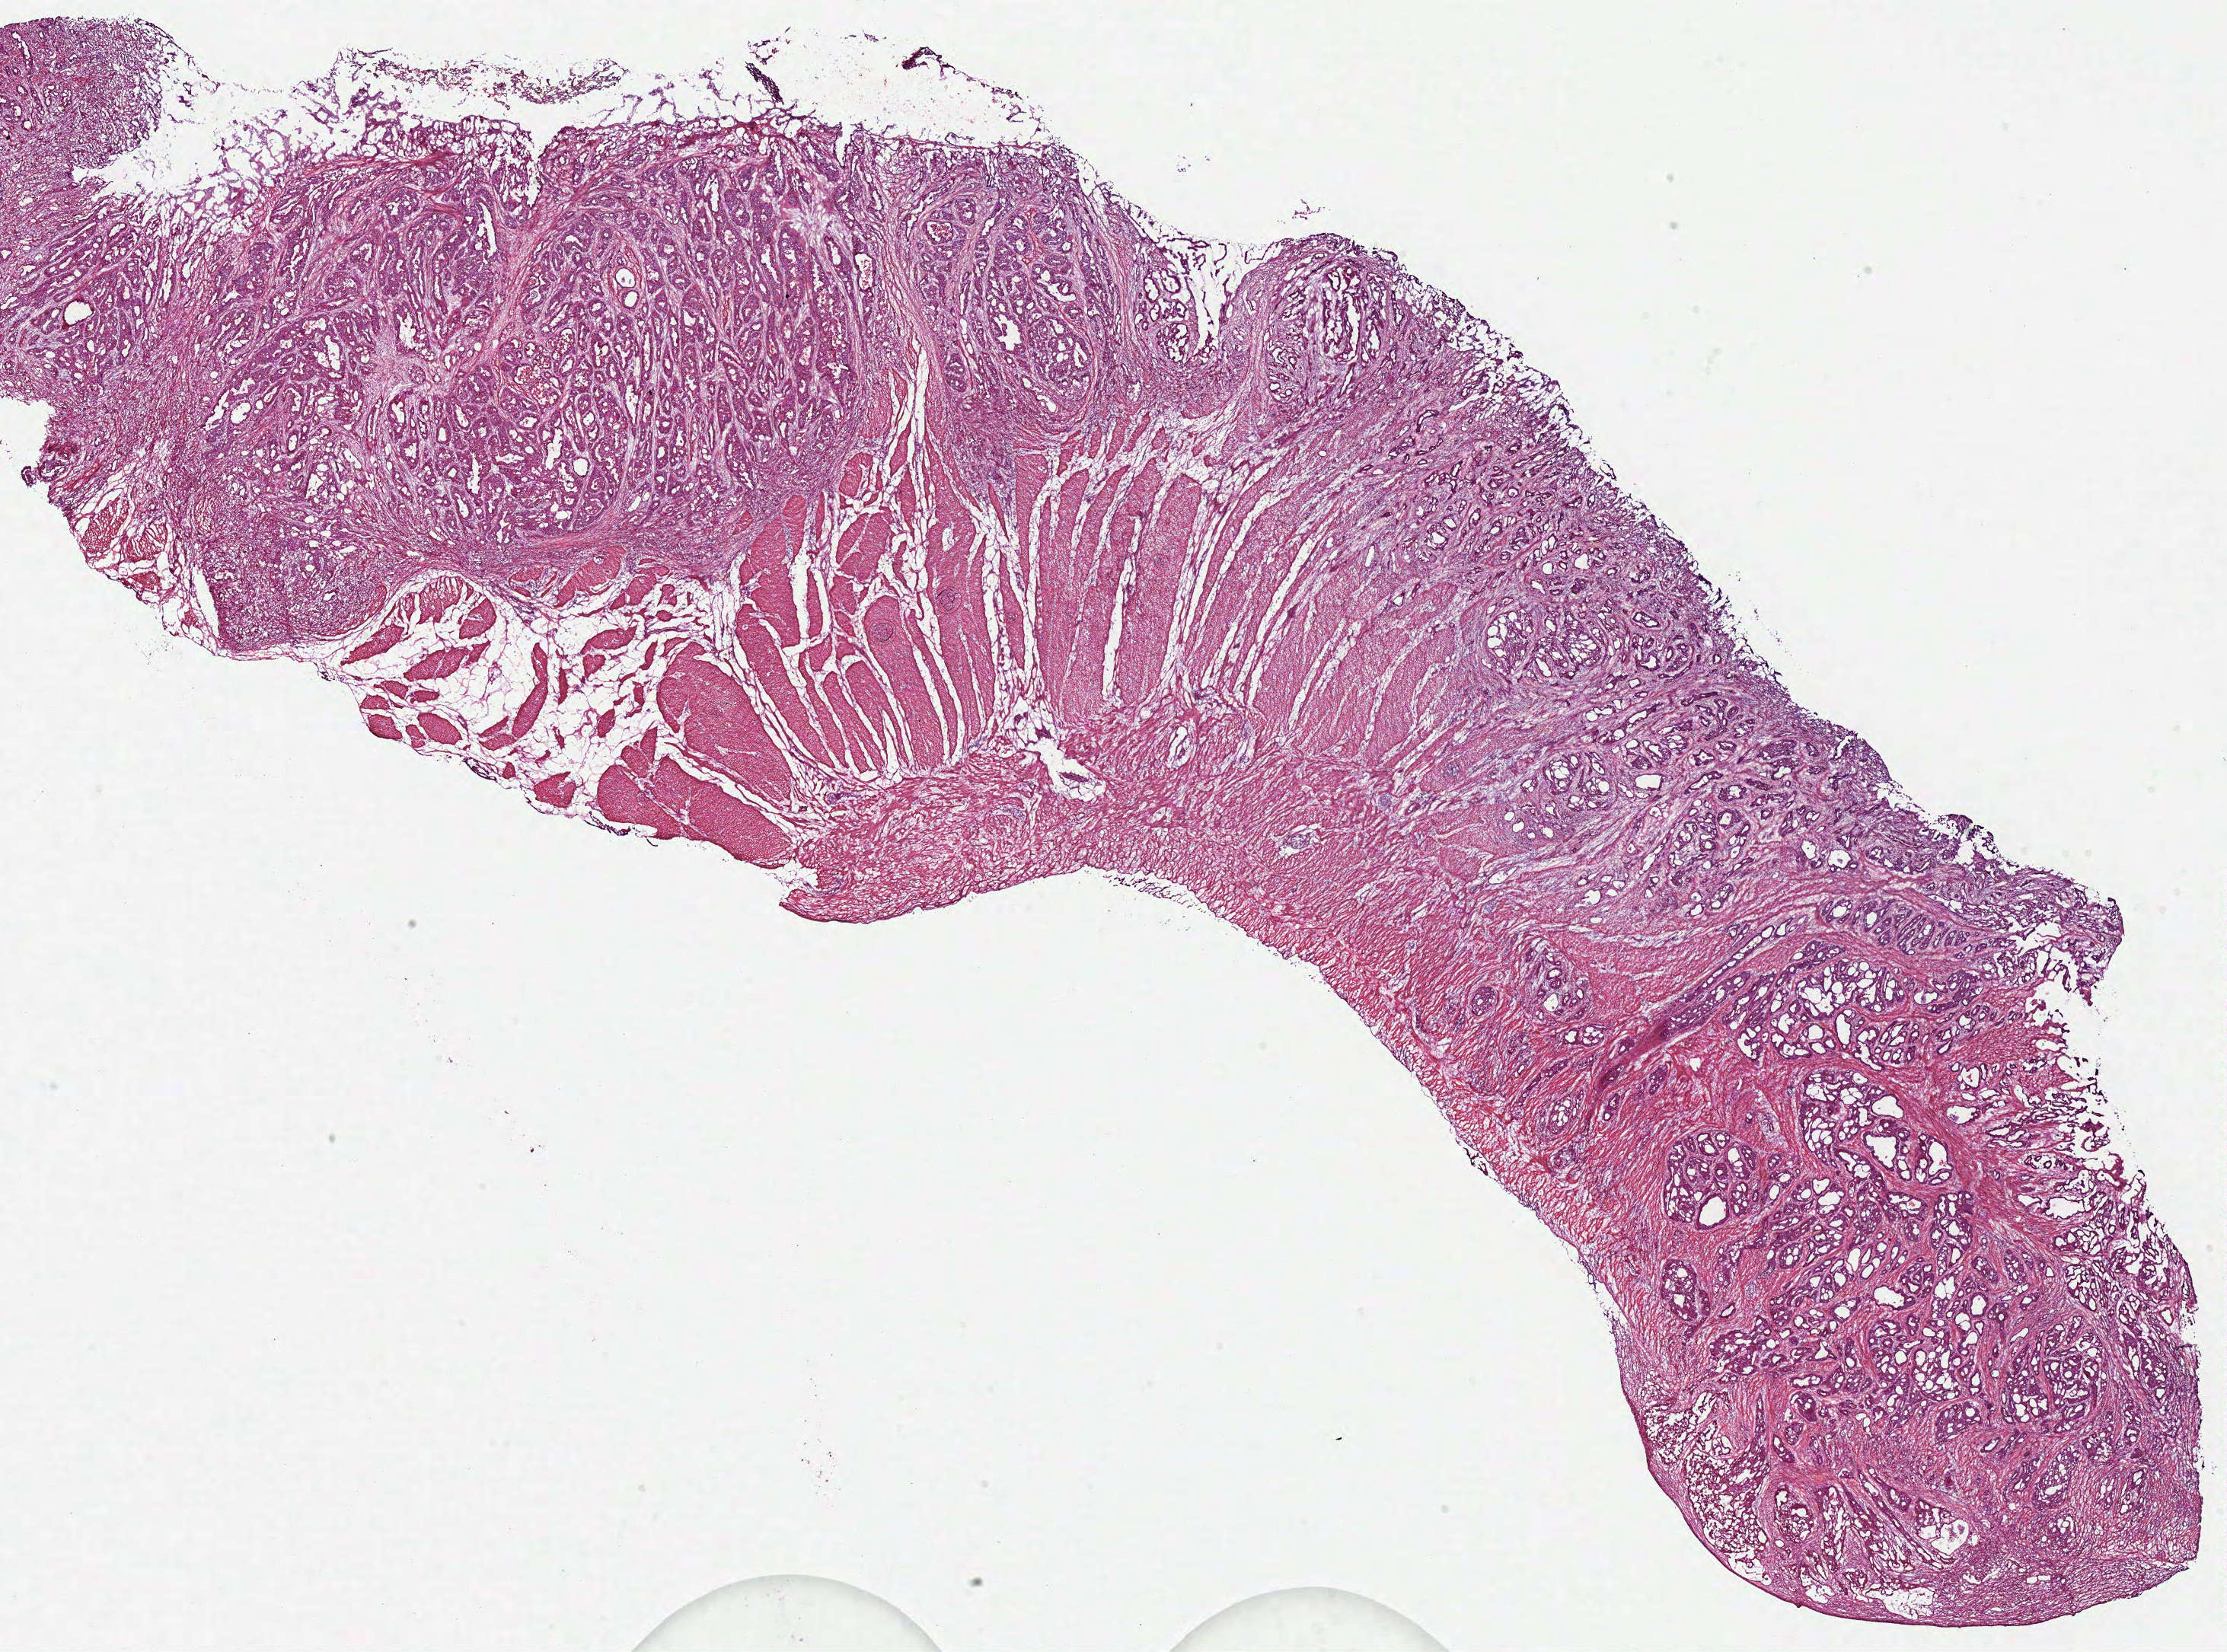
Whole-slide histology image, Hematoxylin and eosin (H&E) stained — low-resolution overview of the scanned area, about 23.0 x 17.1 mm (slide scanned at 40x); frozen section from the top of the tissue portion; primary tumour sample from the stomach. Male patient; age at initial diagnosis 70 years. Histologic grade: G2 (moderately differentiated). Slide review estimates, as recorded: tumour cells 70%, tumour nuclei 75%, normal cells 0%, stromal cells 25%, necrosis 5%.
Pathologic diagnosis: Adenocarcinoma, NOS (body of stomach). TNM: T3 N0 M0. AJCC pathologic stage: IIA (7th edition). Lymph nodes positive (case pathology): 0 of 8 examined.